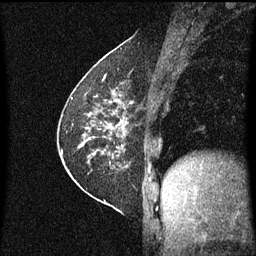
Breast MRI (dynamic contrast-enhanced), one sagittal slice. Slice 25 of 60 in the series (ordered by position). Dynamic contrast-enhanced series, image 2 of 3 at this slice position (ordered by acquisition). 1.5 T. TE 4.2 ms, TR 8.4 ms. 2 mm slice thickness. 256 × 256 image matrix, field of view 200 × 200 mm. Patient: female, 60 years.
Structures marked on this image (semi-automatically segmented with operator editing):
- analysis volume of interest (the breast-tissue region the enhancement analysis was run in; not a lesion): bounding box <69,66,133,193> (left, top, right, bottom; pixels)
- tumour enhancement mask (voxels above the 70 % enhancement threshold inside the analysis volume of interest): <71,84,132,167>